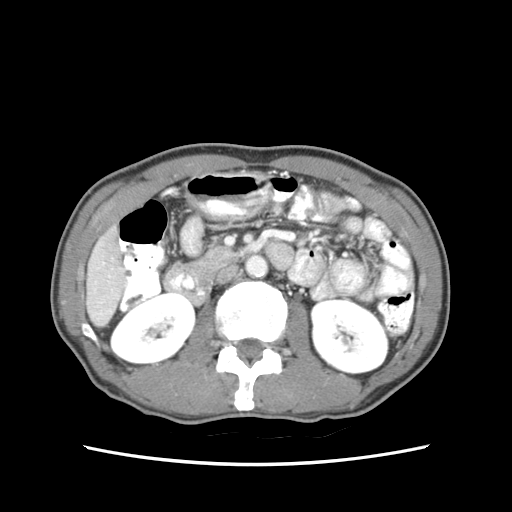
Contrast-enhanced abdominal CT (liver protocol), one axial slice. Position 16 of 79 along the scan axis. Soft-tissue window (W 400 / L 40 HU). 2.5 mm slice thickness. 512 × 512 image matrix, field of view 320 × 320 mm. Case-level facts recorded for this patient, not image findings: diagnosis: hepatocellular carcinoma (patient treated with transarterial chemoembolisation; whether this scan precedes or follows treatment is not stated here); TNM stage (as recorded): Stage-IIIB; Child-Pugh class: A; tumour differentiation: moderately differentiated; tumour nodularity: multinodular.
Outlined on this slice (semi-automatically segmented with operator editing):
- liver parenchyma outside the tumour (the mass and vessels are separate outlines, so this box may not span the whole liver): bounding box (x1, y1, x2, y2) in pixels: (86, 226, 126, 326)
- liver vessels: (94, 256, 115, 270)